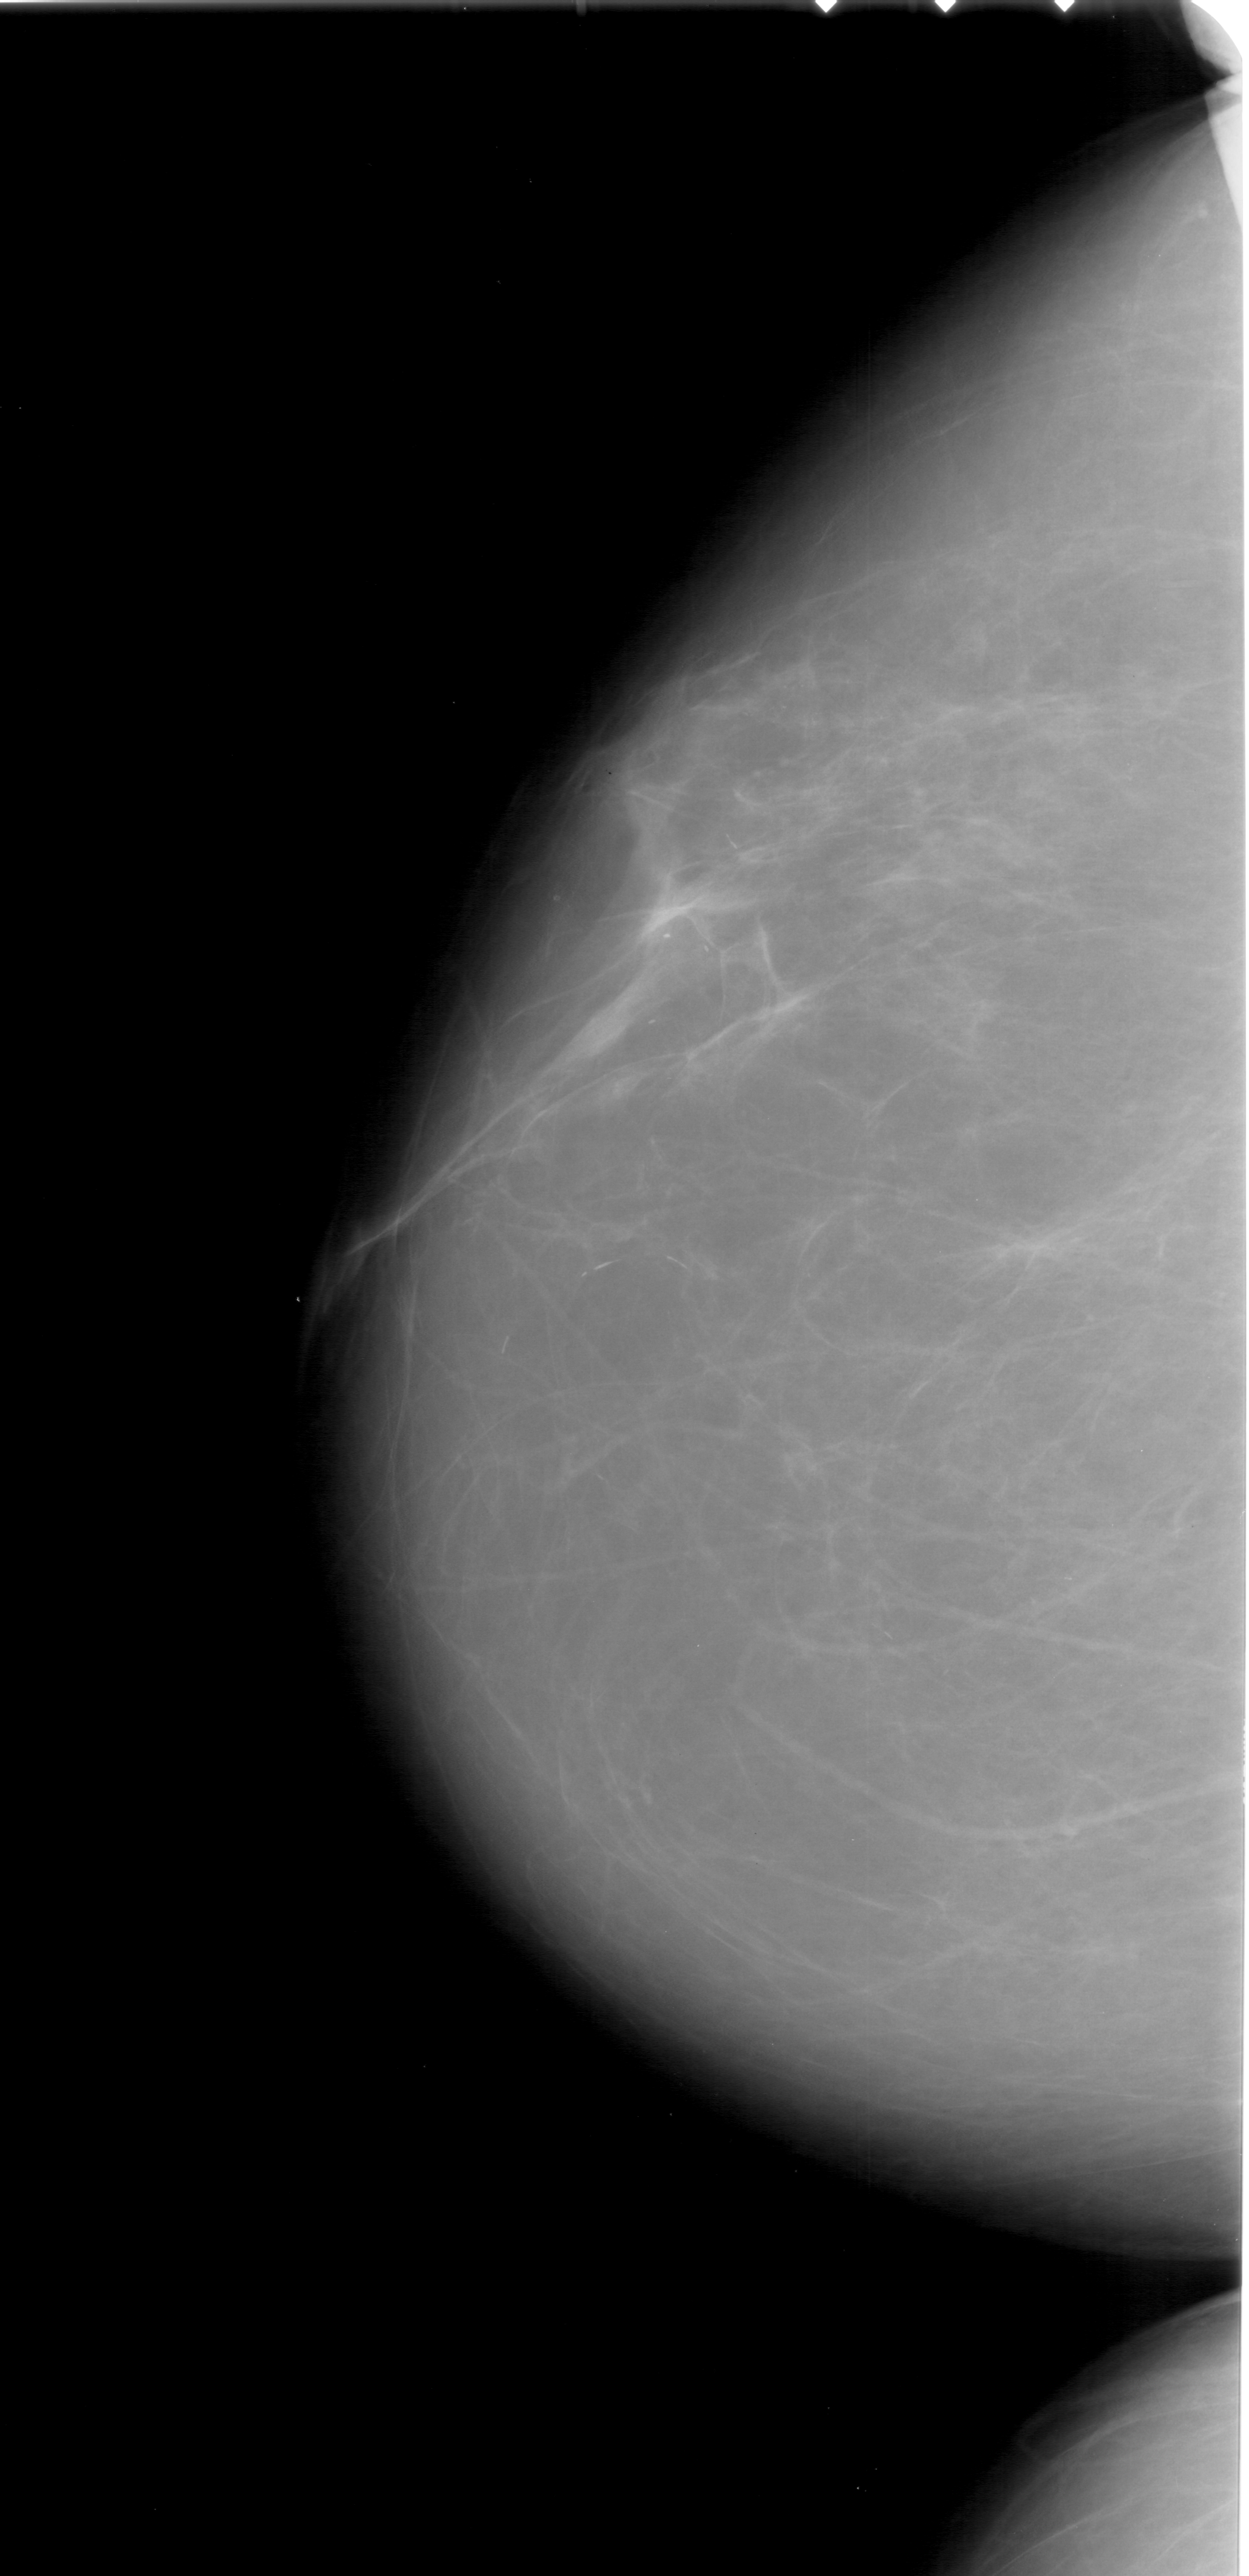
Mammogram (digitized film), left breast, CC view, BI-RADS breast density category 2 (scale 1–4).
Marked findings (only marked abnormalities are described; nothing is implied about the rest of the image): calcifications, morphology pleomorphic, distribution clustered; BI-RADS assessment category 4; subtlety rating 2 on a 1 (subtle) to 5 (obvious) scale; pathology (as recorded): malignant.